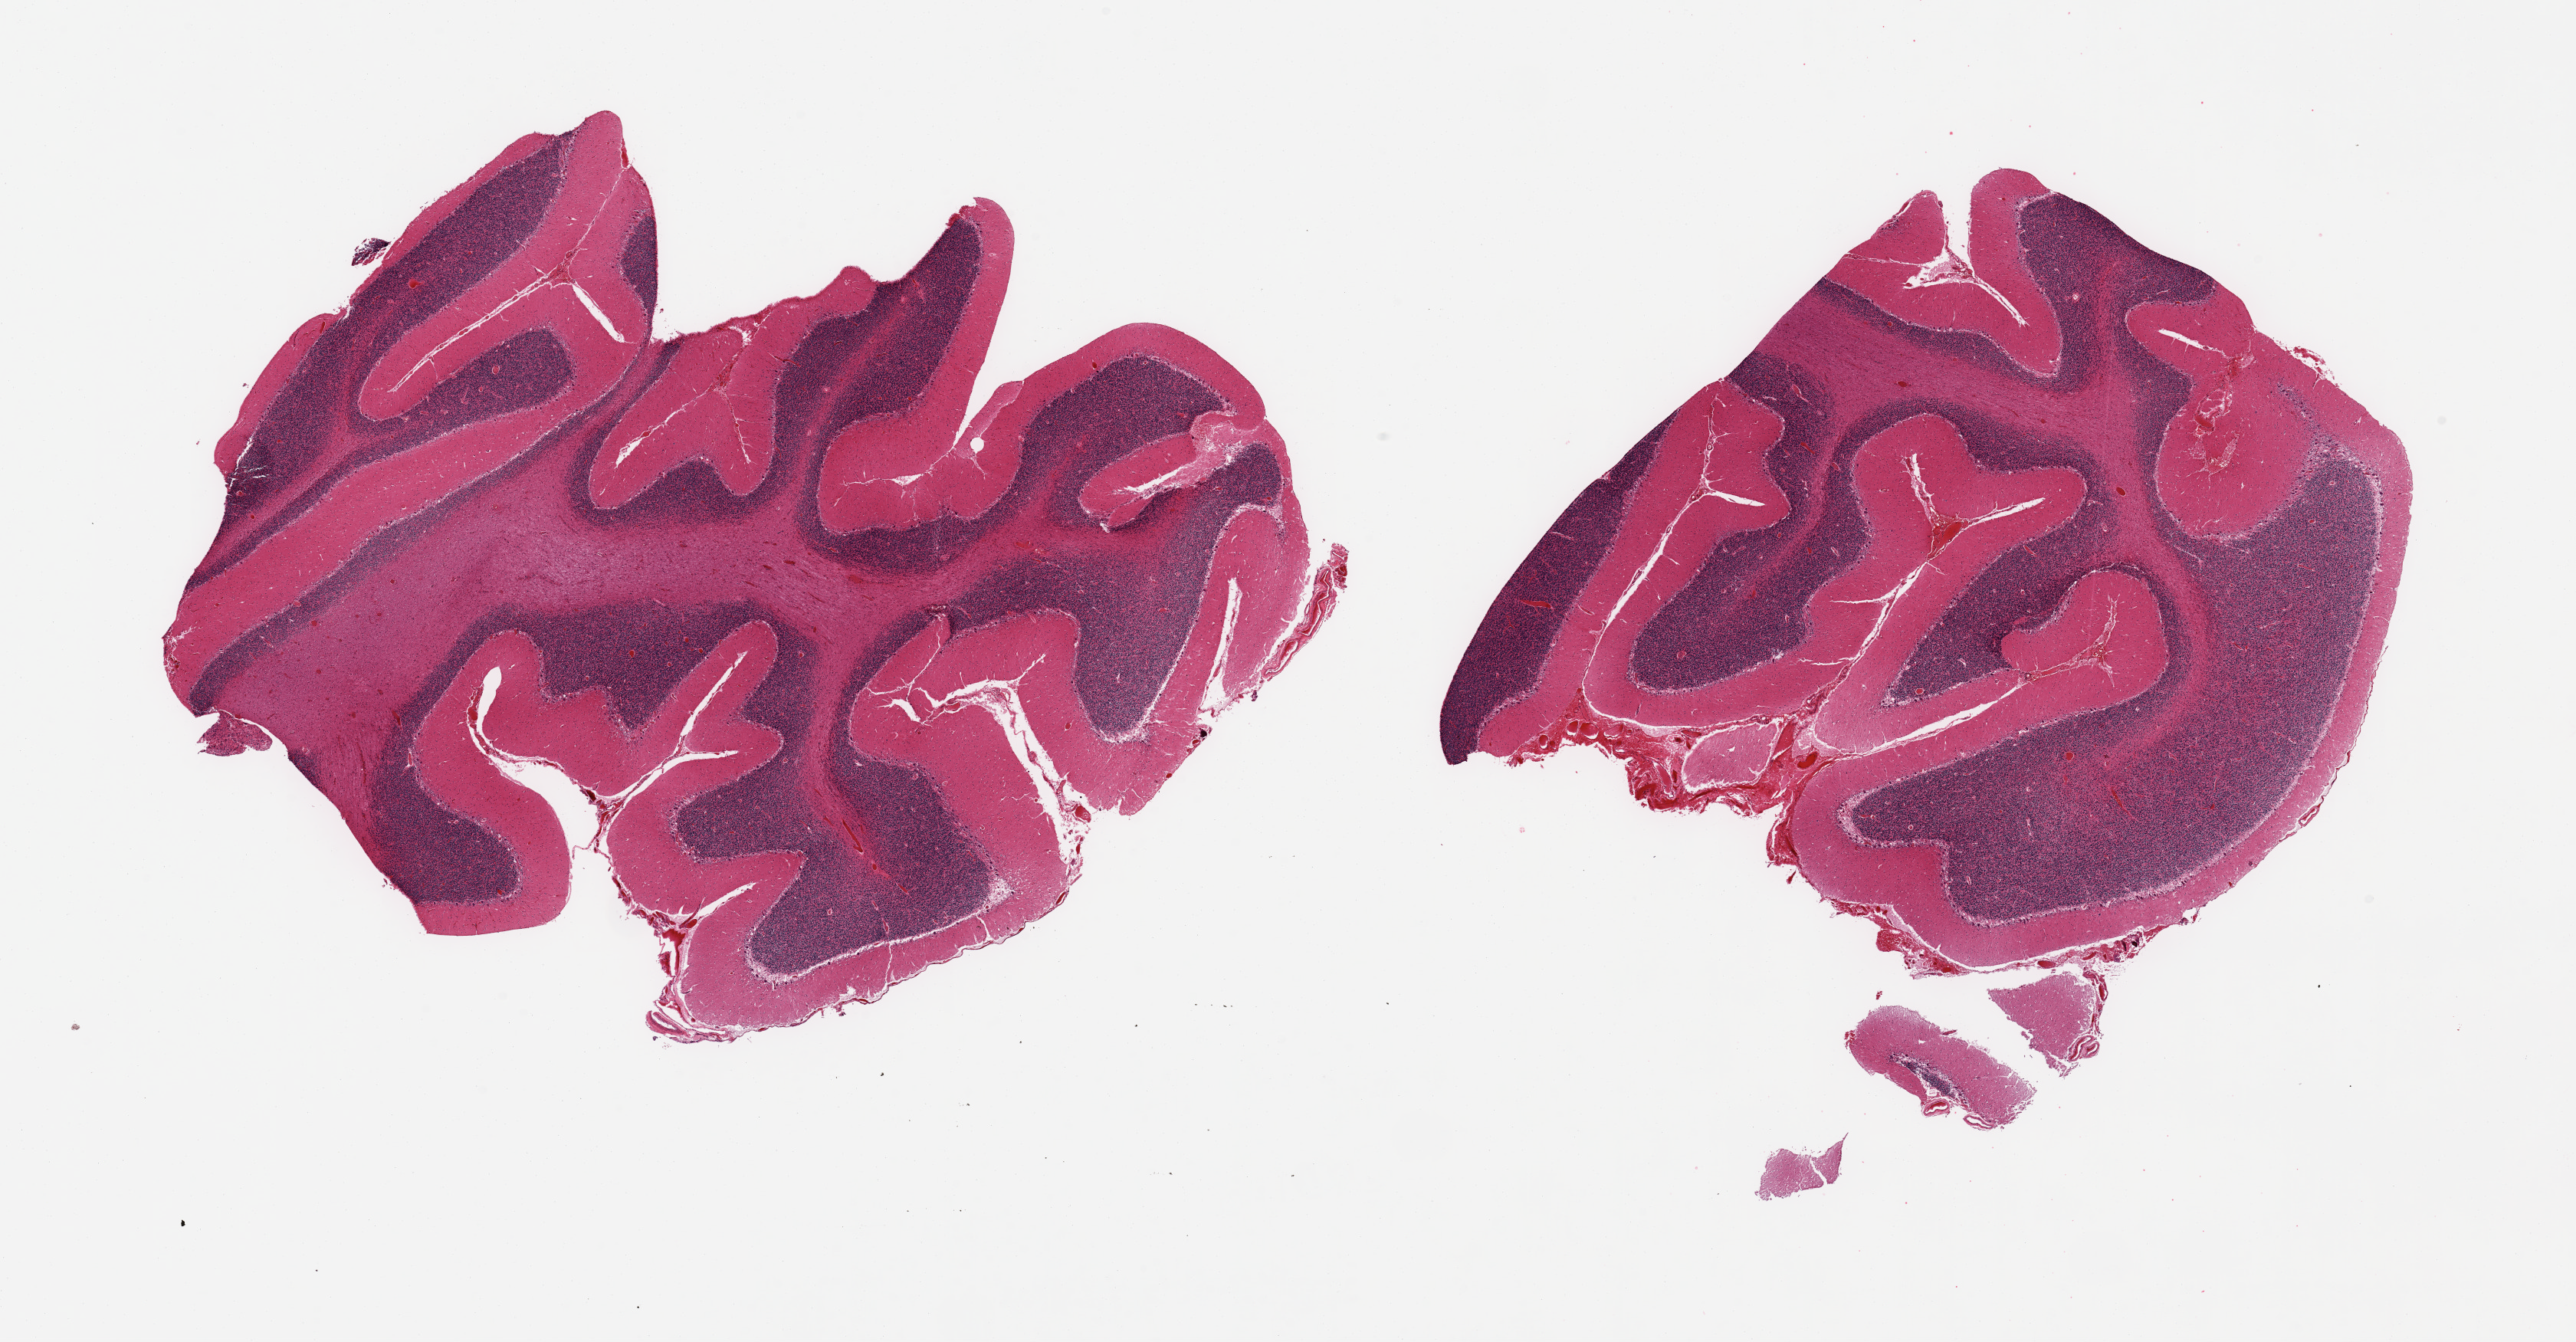
Digitized H&E-stained section, shown as a low-resolution overview of the whole scanned area (about 26.6 x 13.8 mm); PAXgene-fixed paraffin-embedded (PFPE) section; sampled site (target tissue): cerebellum; tissue donor sample. Donor sex: male.
Reviewer comment on this tissue sample: 2 pieces, no abnormalities.